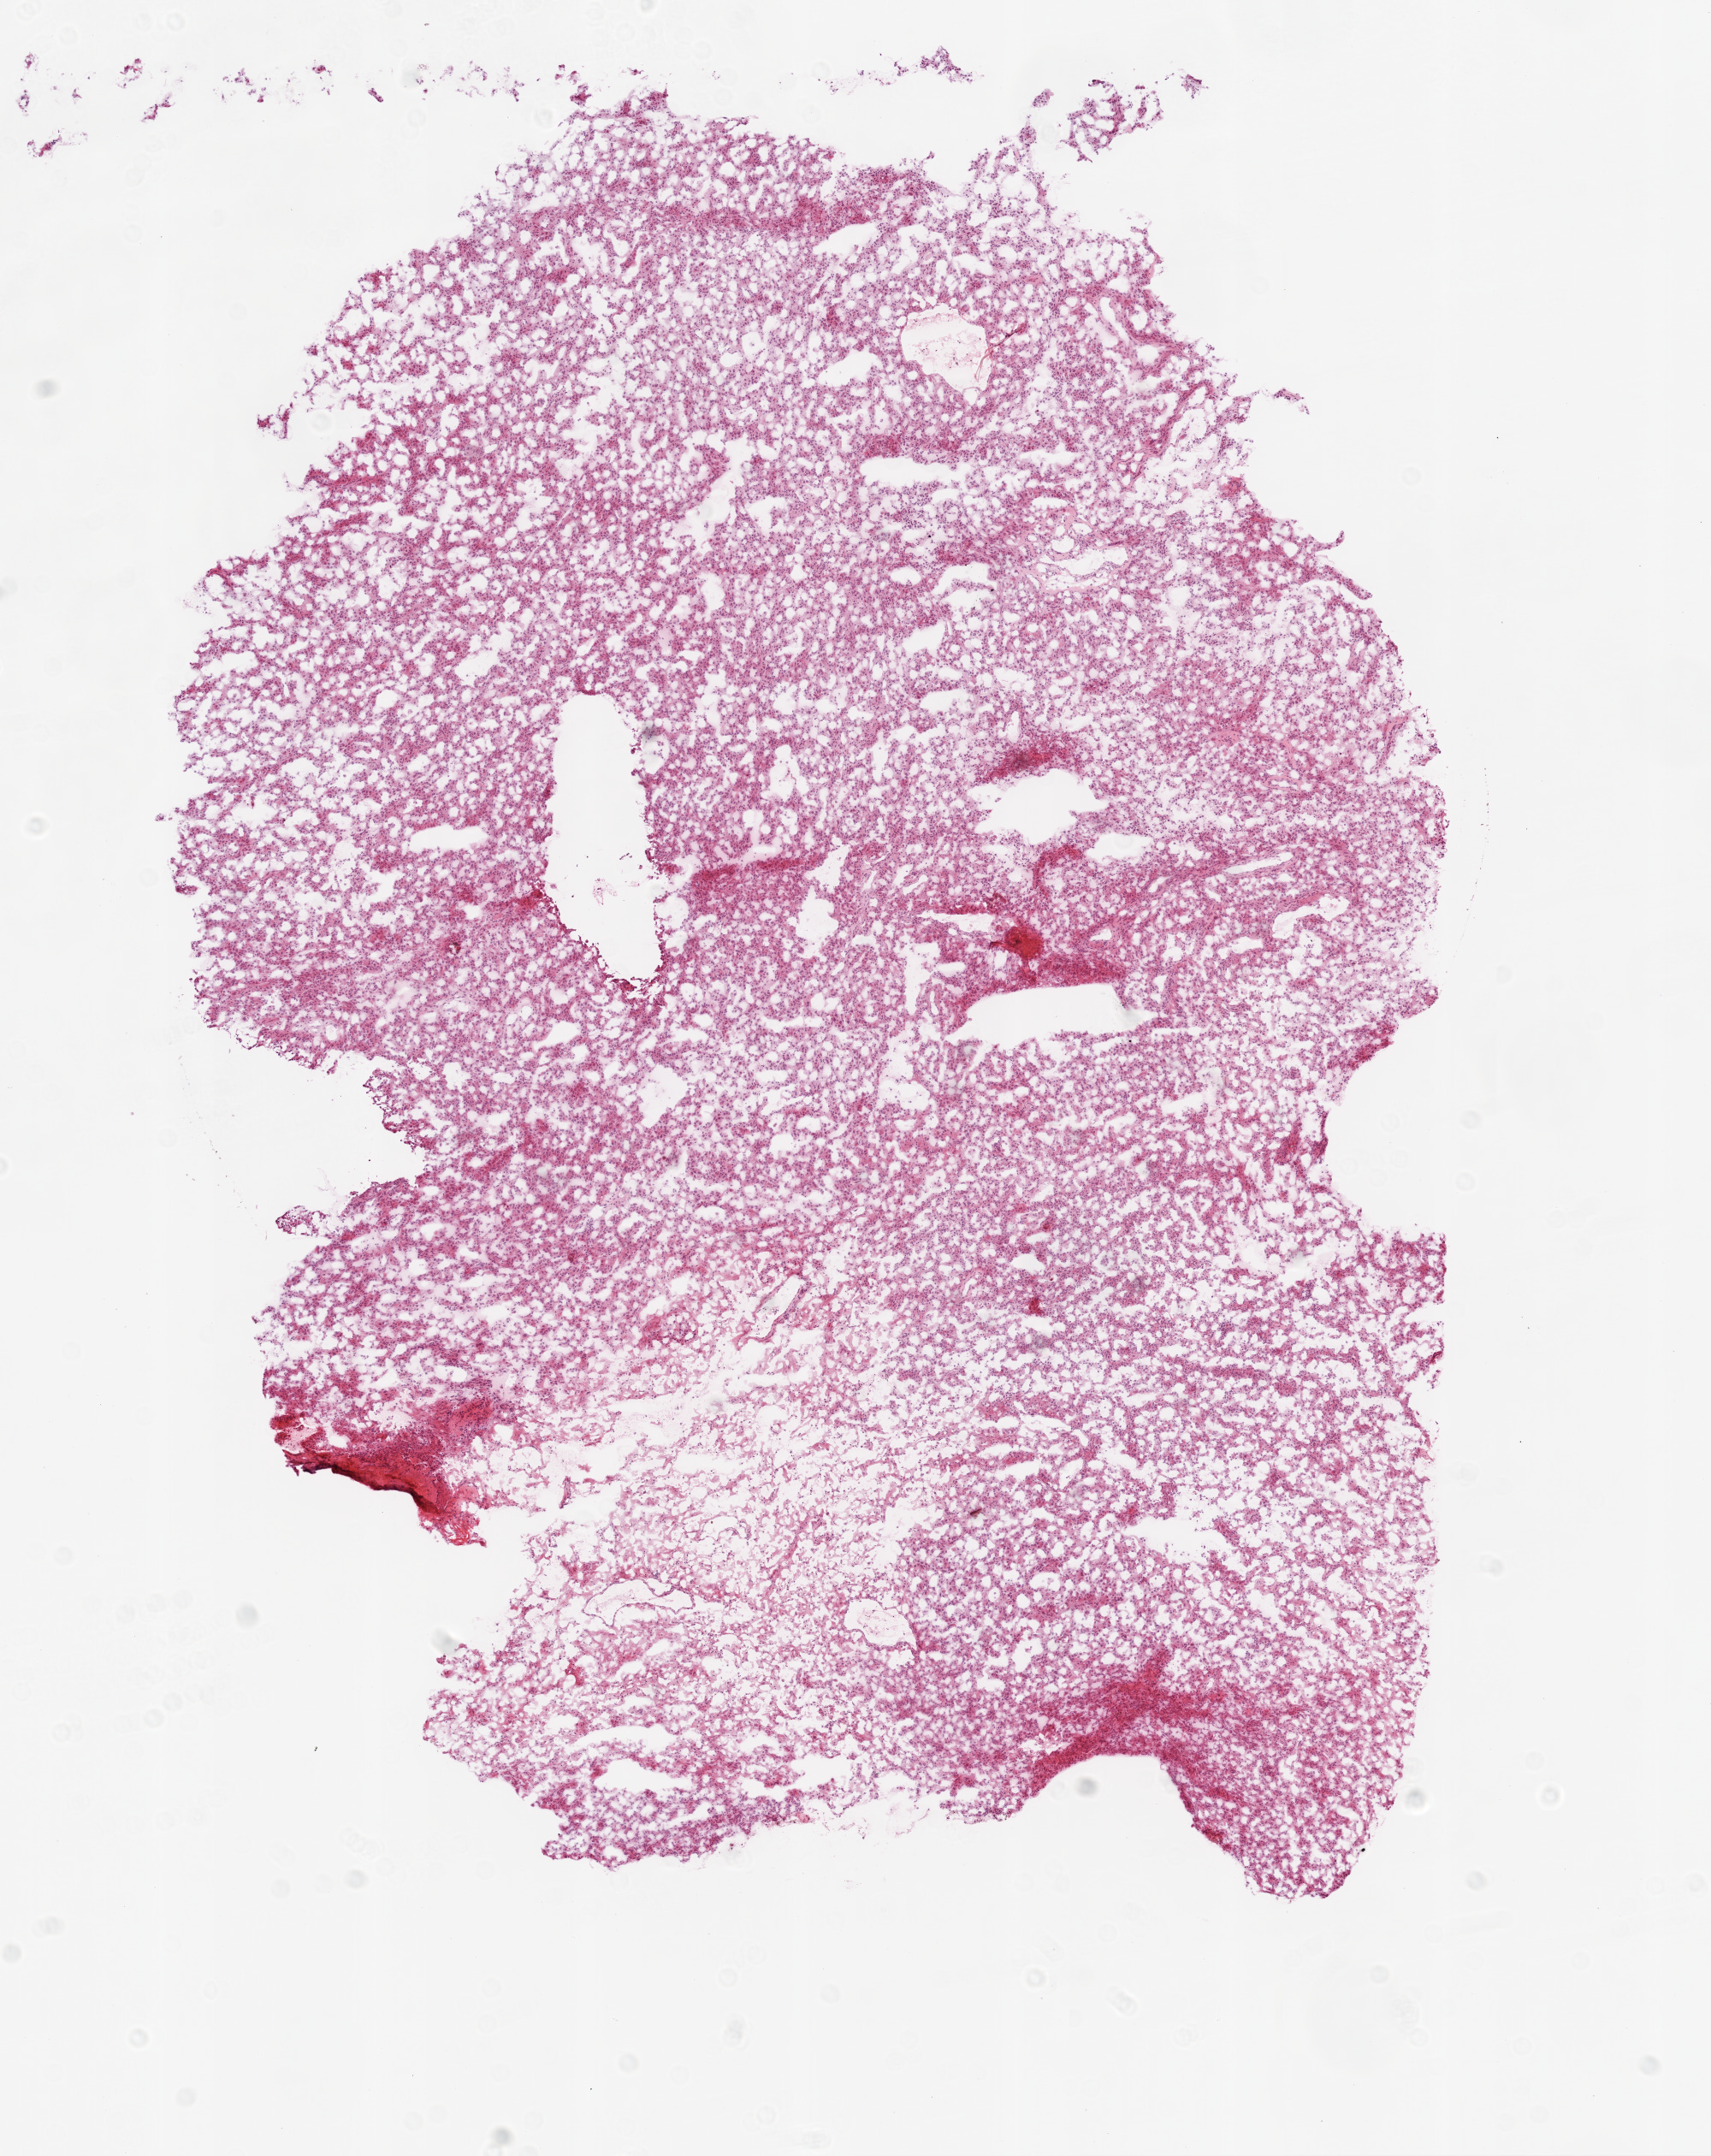
Whole-slide histology image, Hematoxylin and eosin (H&E) stained, whole scanned area (about 8.0 x 10.1 mm) shown as a low-resolution overview, frozen section, primary tumour sample from the brain. Patient: female, age at initial diagnosis 59 years. Composition of this section per pathologist review: tumour cells 95%, tumour nuclei 95%, normal cells 0%, stromal cells 0%, necrosis 5%.
• diagnosis: Glioblastoma